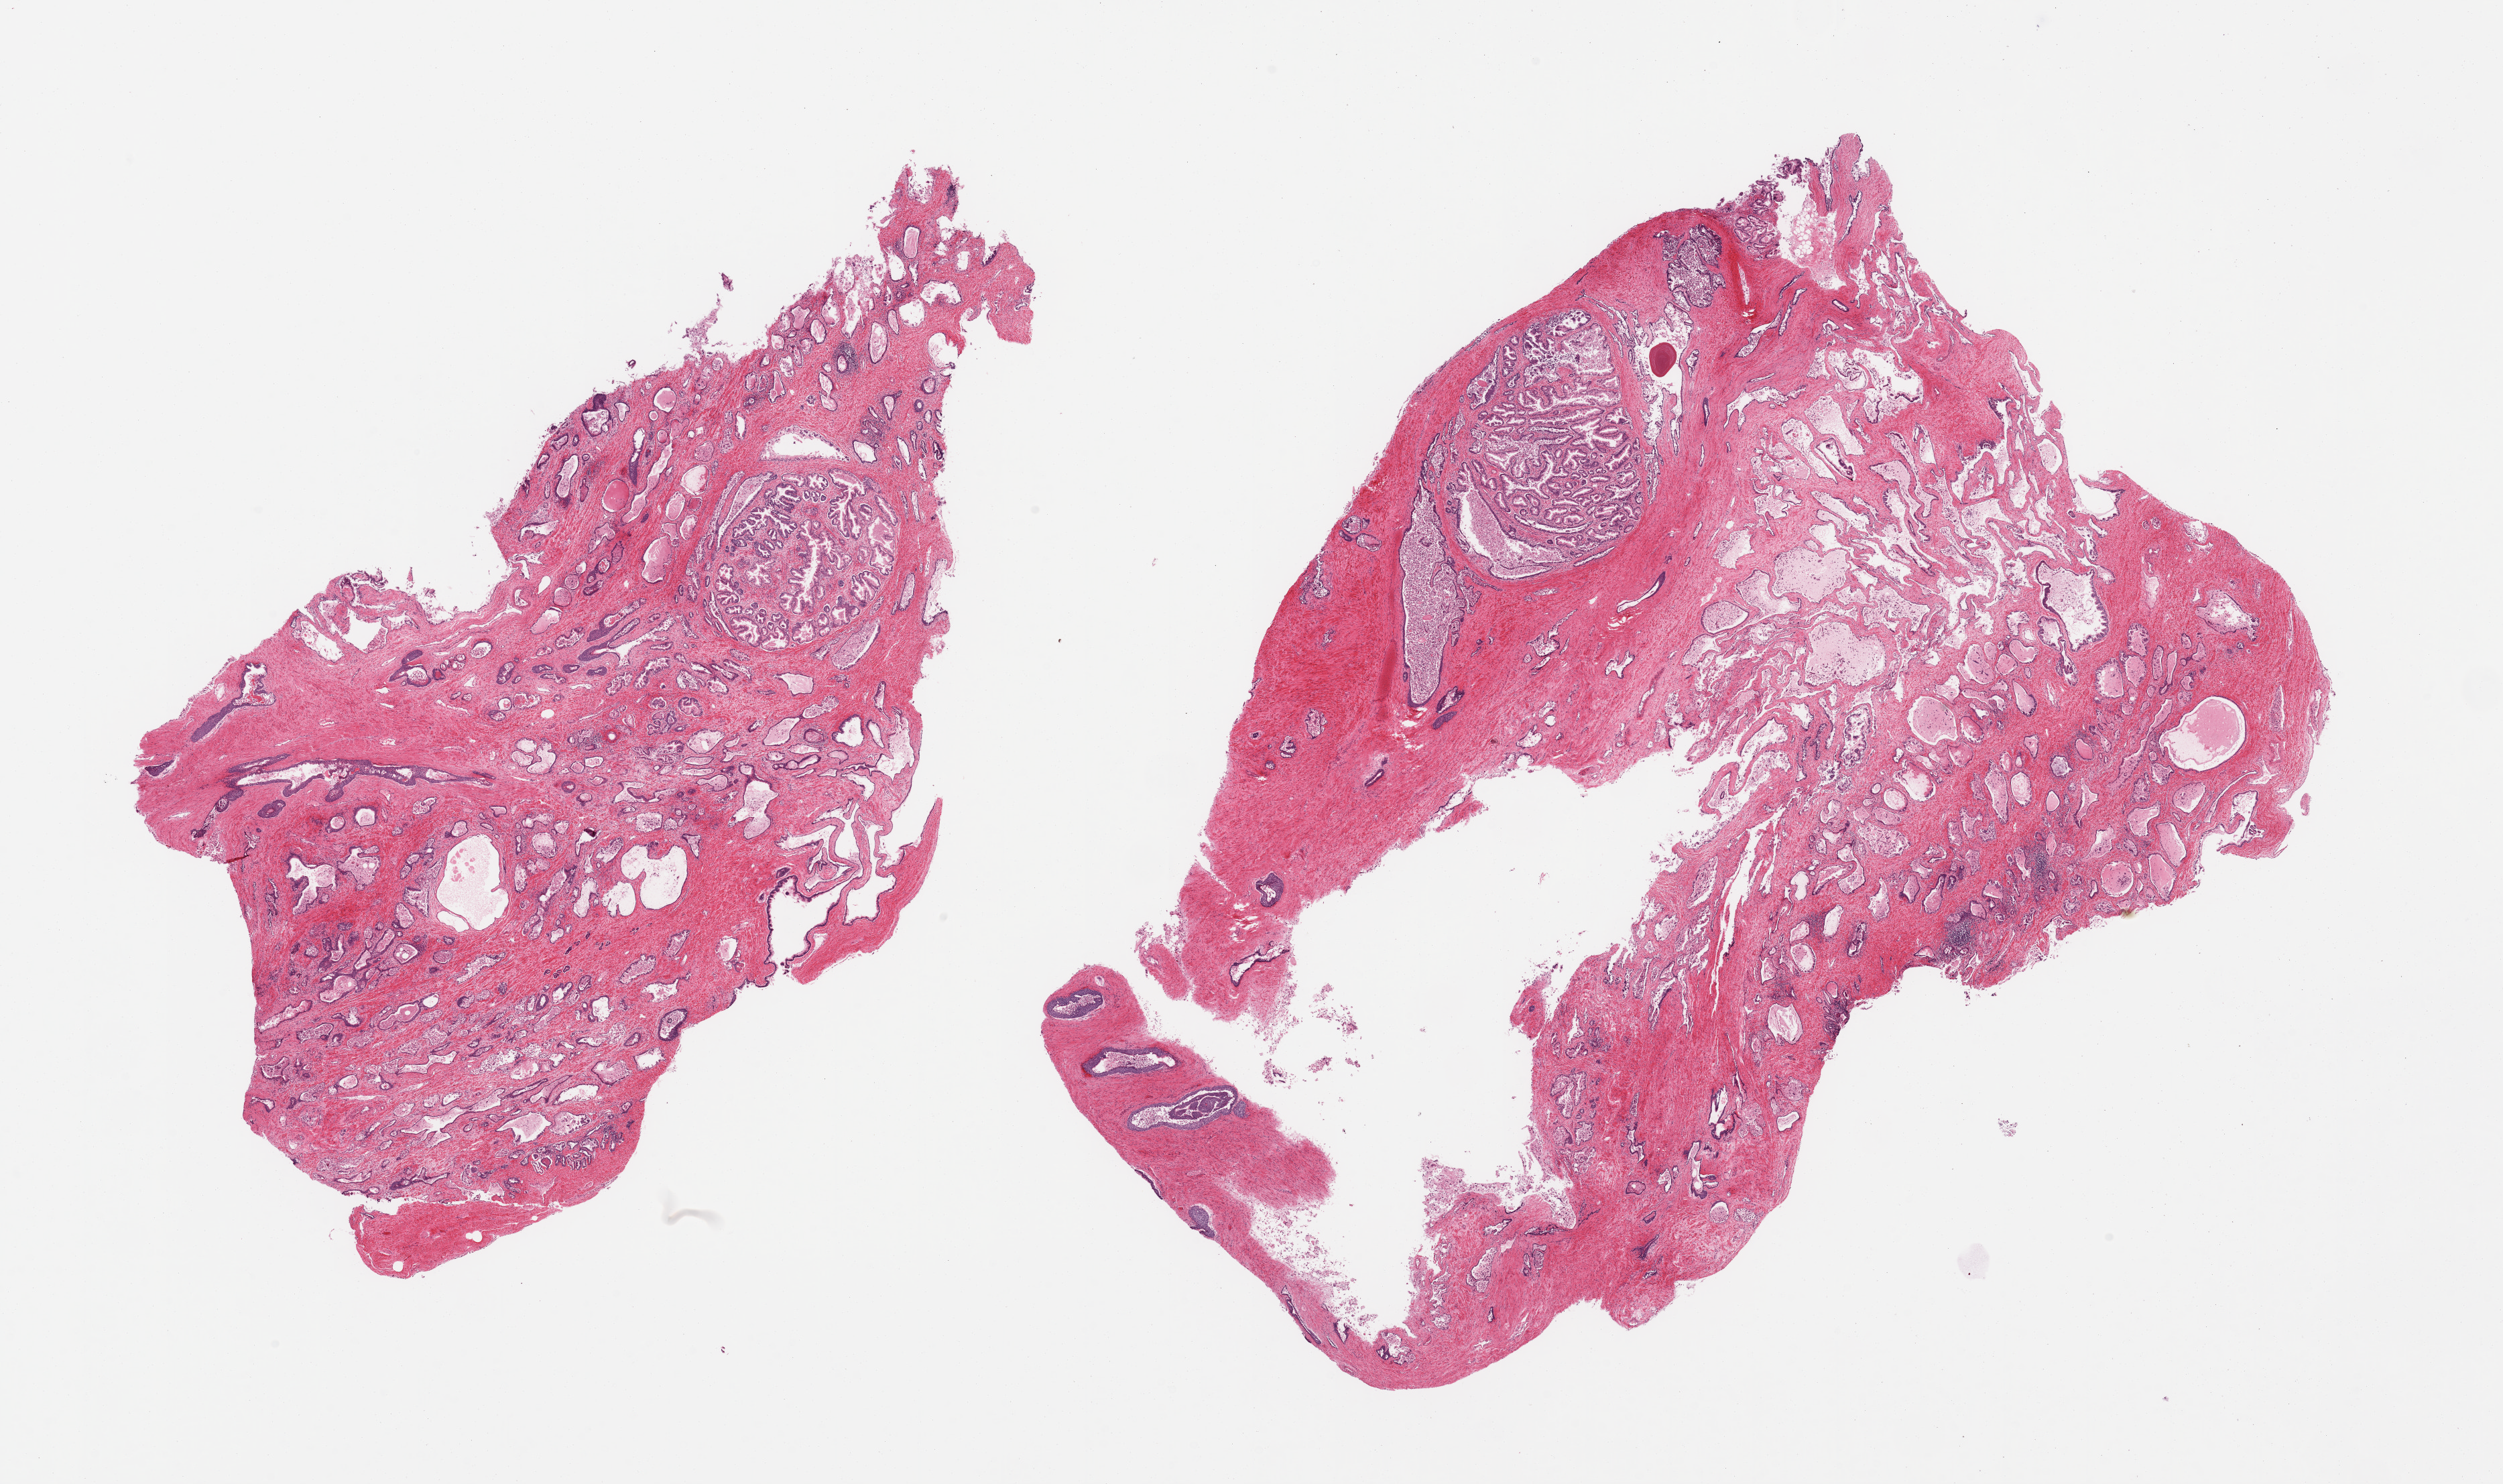
Whole-slide image, haematoxylin and eosin stain, whole scanned area (about 29.5 x 17.5 mm) shown as a low-resolution overview, PAXgene-fixed, paraffin-embedded tissue, target tissue: prostate, tissue donor sample. Donor: male.
Pathologist's review note for this sample: 2 pieces: nodular hyperplasia.